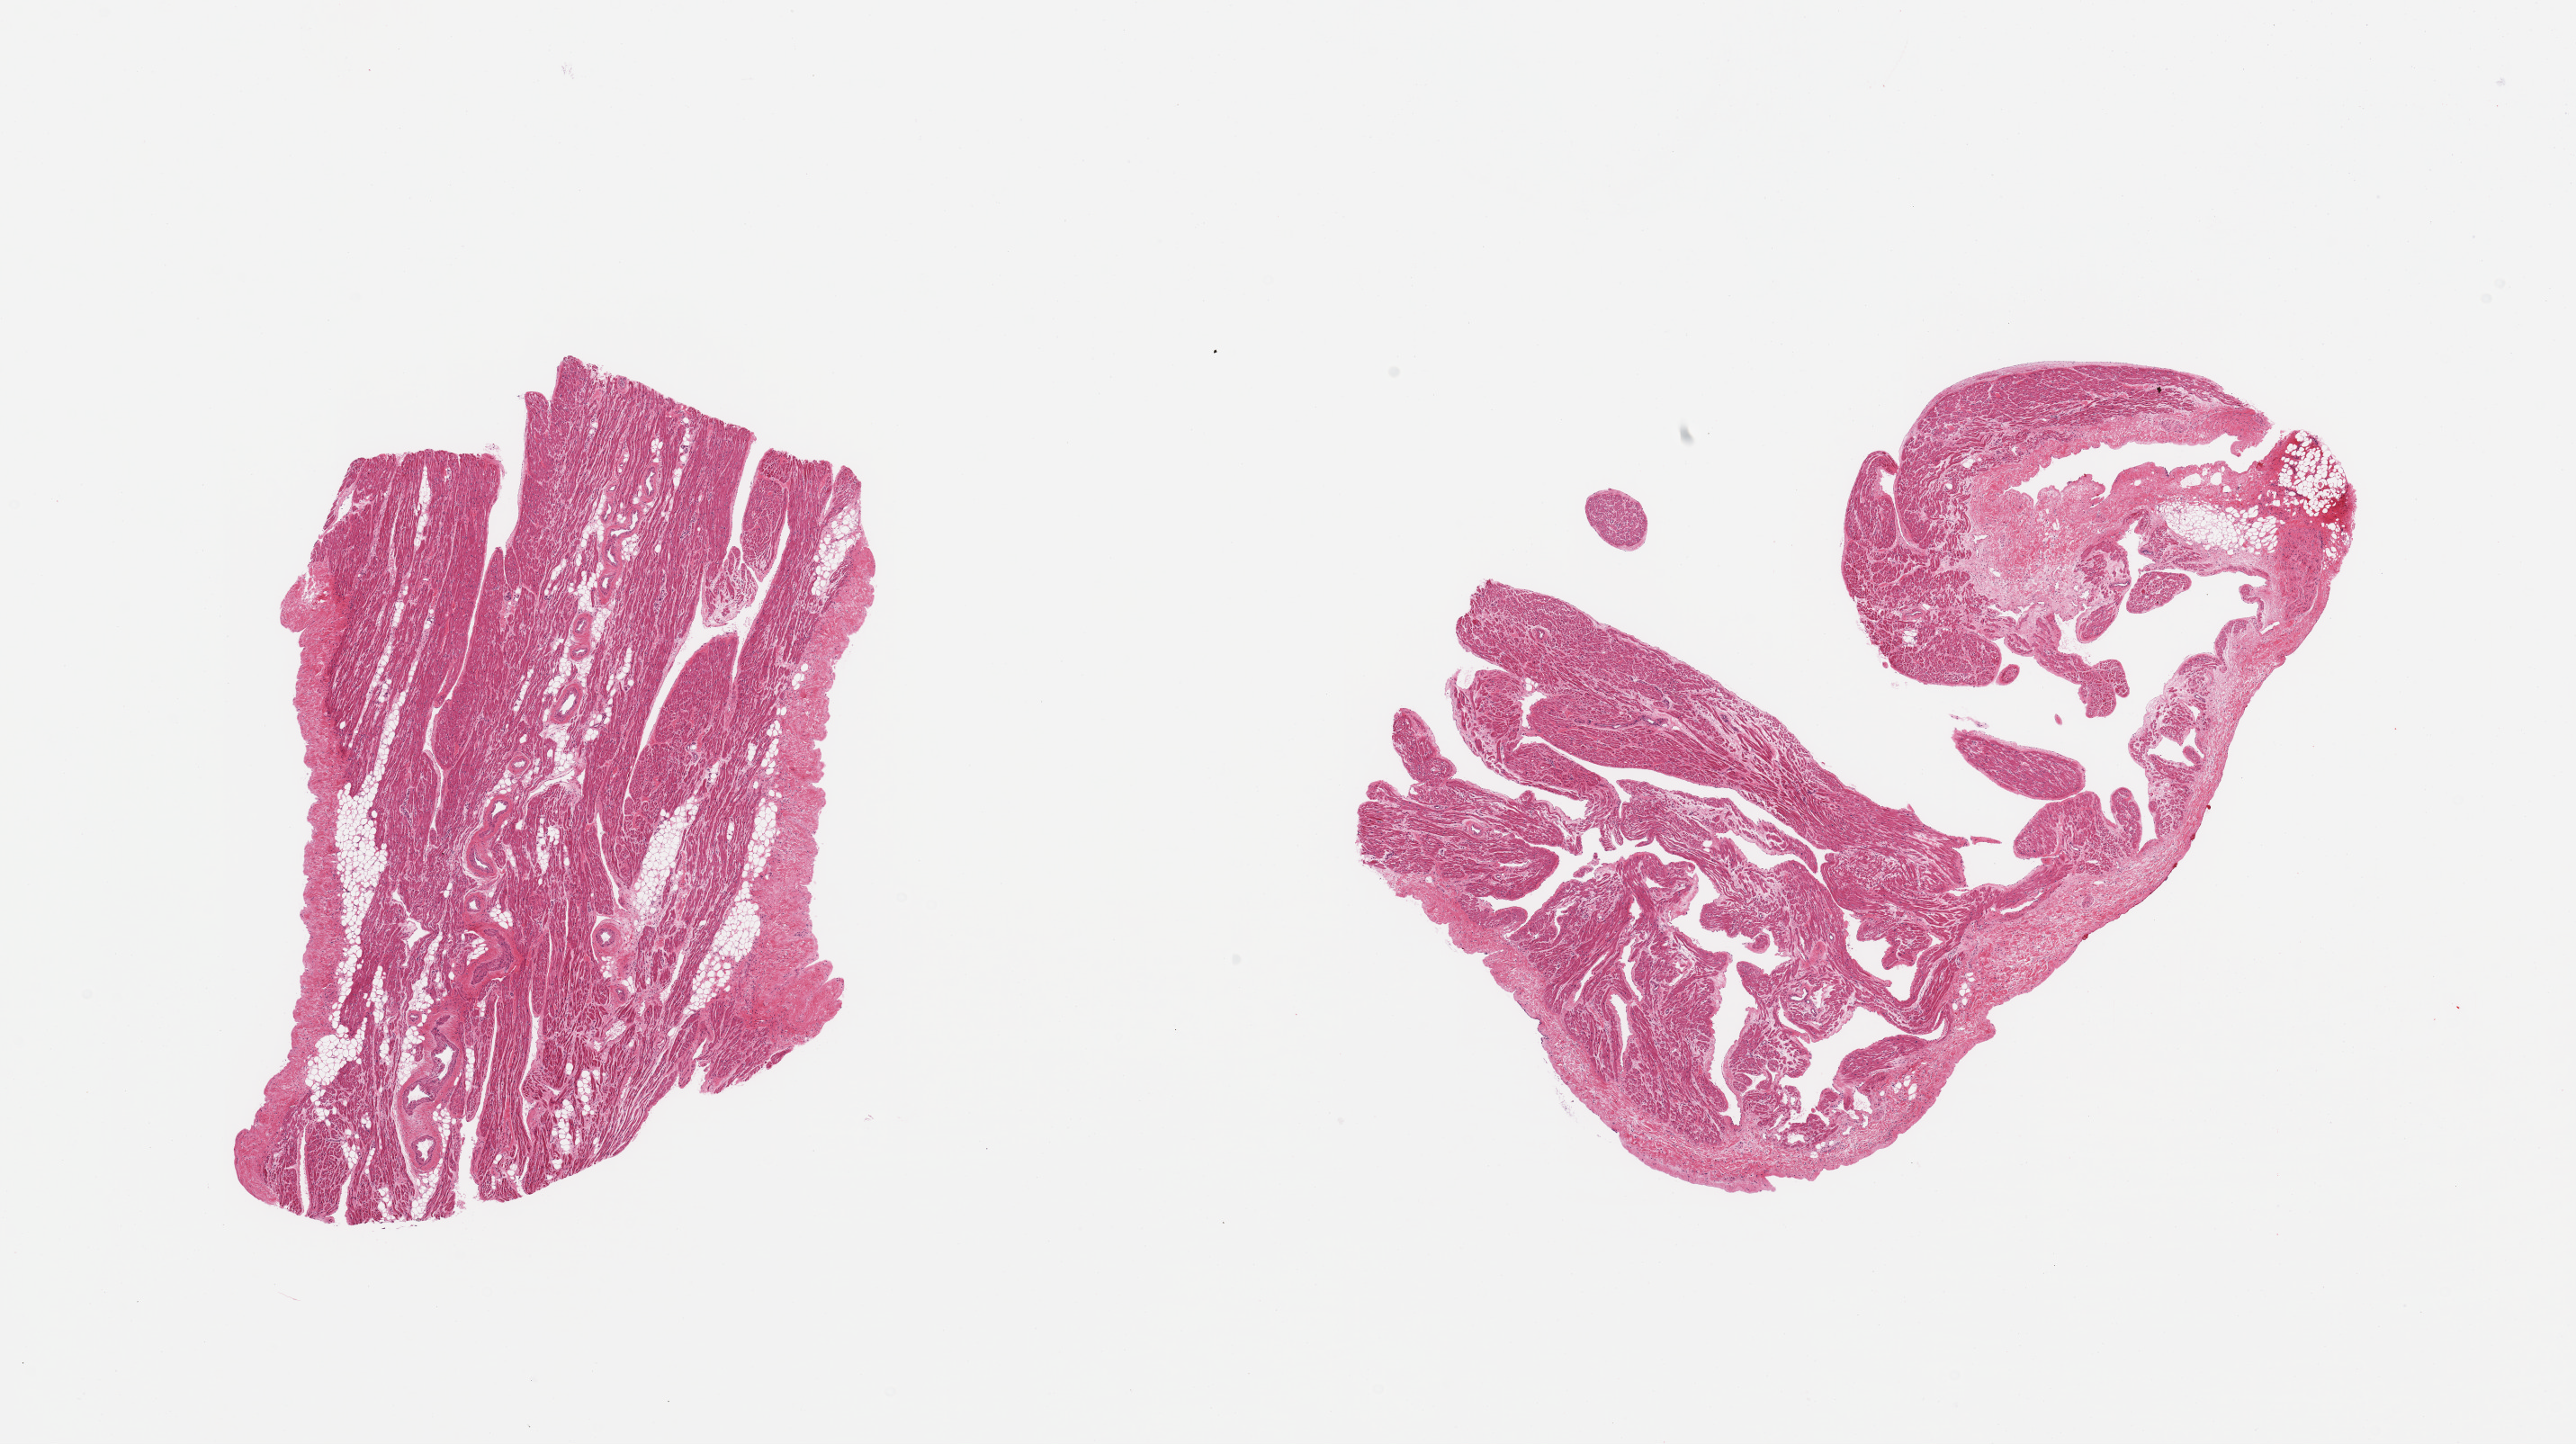
H&E whole-slide image — a low-resolution overview of the entire scanned area, about 22.6 x 12.7 mm (from a 20x scan); PAXgene-fixed, paraffin-embedded tissue; target tissue: auricular appendage; donor tissue sample.
Reviewer comment on this tissue sample: 2 pieces, no abnormalities.